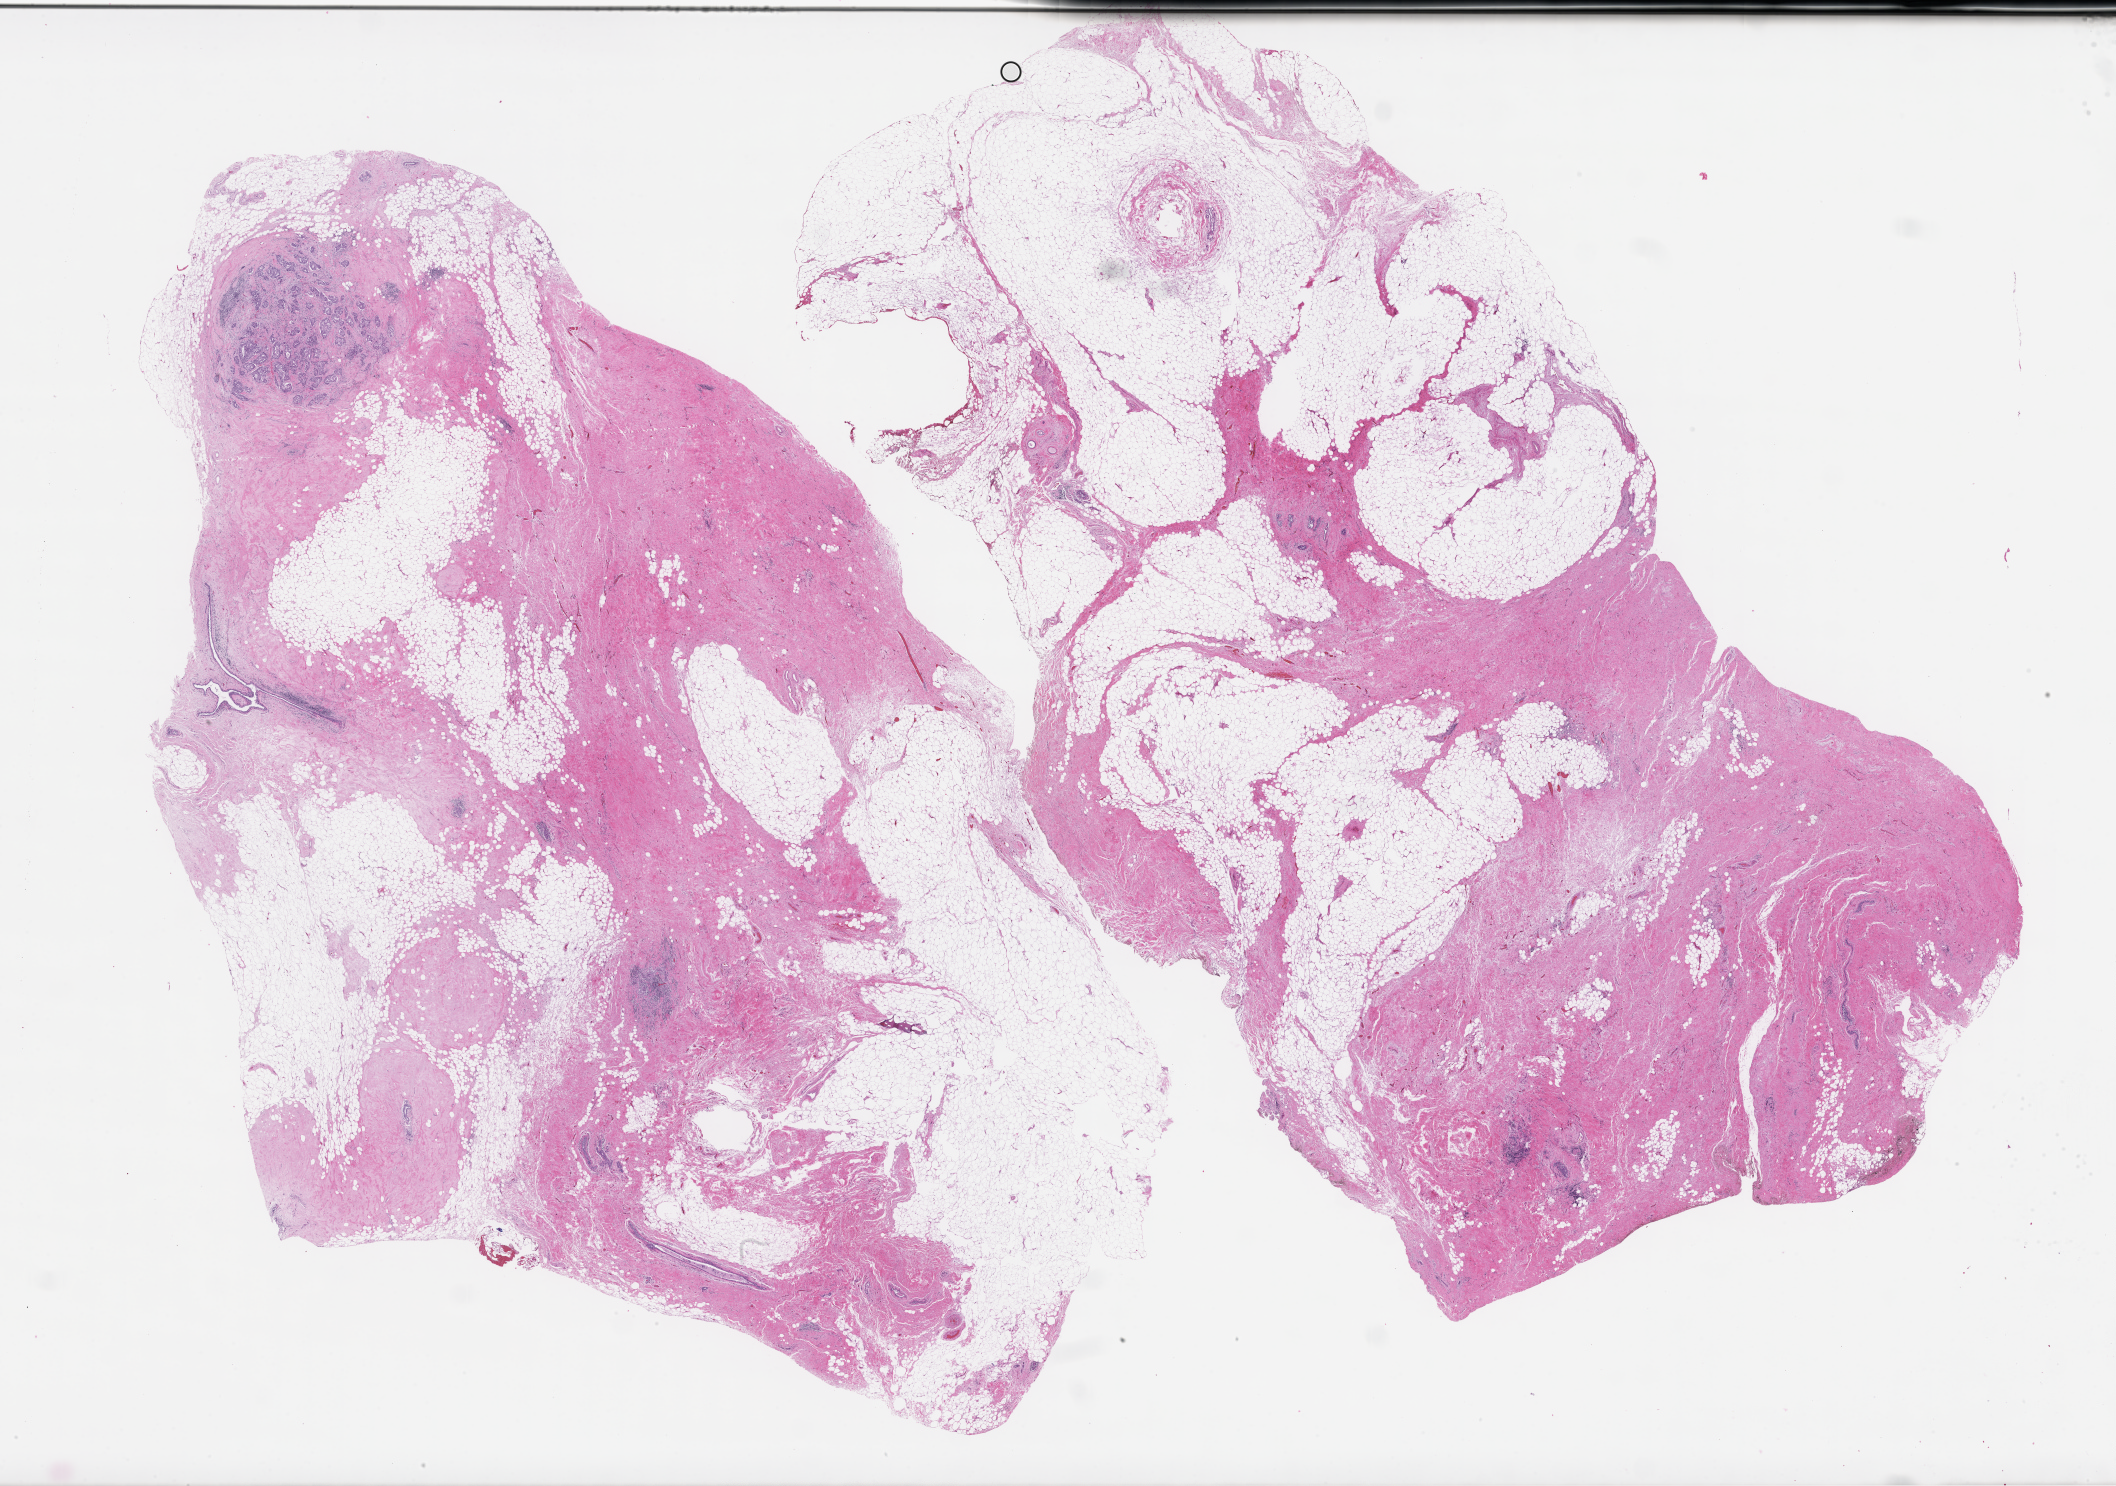
Digitized hematoxylin and eosin (H&E)-stained section, low-resolution overview of the scanned area, about 34.2 x 24.0 mm, formalin-fixed paraffin-embedded section, tissue site: breast, collected on treatment. Female patient.
This section: primary tumour tissue. Diagnosis: Invasive Breast Carcinoma.